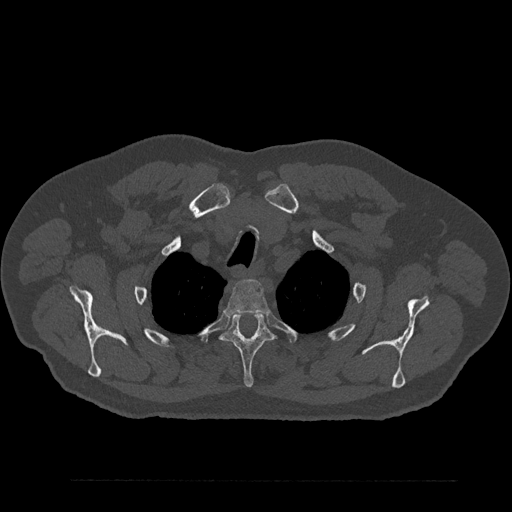
CT including the spine, one axial slice; reconstruction kernel Br40s/3; bone window (W 1800 / L 400 HU); 512 × 512 image matrix, field of view 430 × 430 mm. Patient: male, 61 years. From the clinical record (not read from this slice): primary cancer: prostate.
Annotated regions visible in this slice (semi-automatically segmented with operator editing):
- T2 vertebra: bounding box (x1, y1, x2, y2) in pixels: (225, 279, 269, 316)
- T3 vertebra: (221, 313, 274, 388)